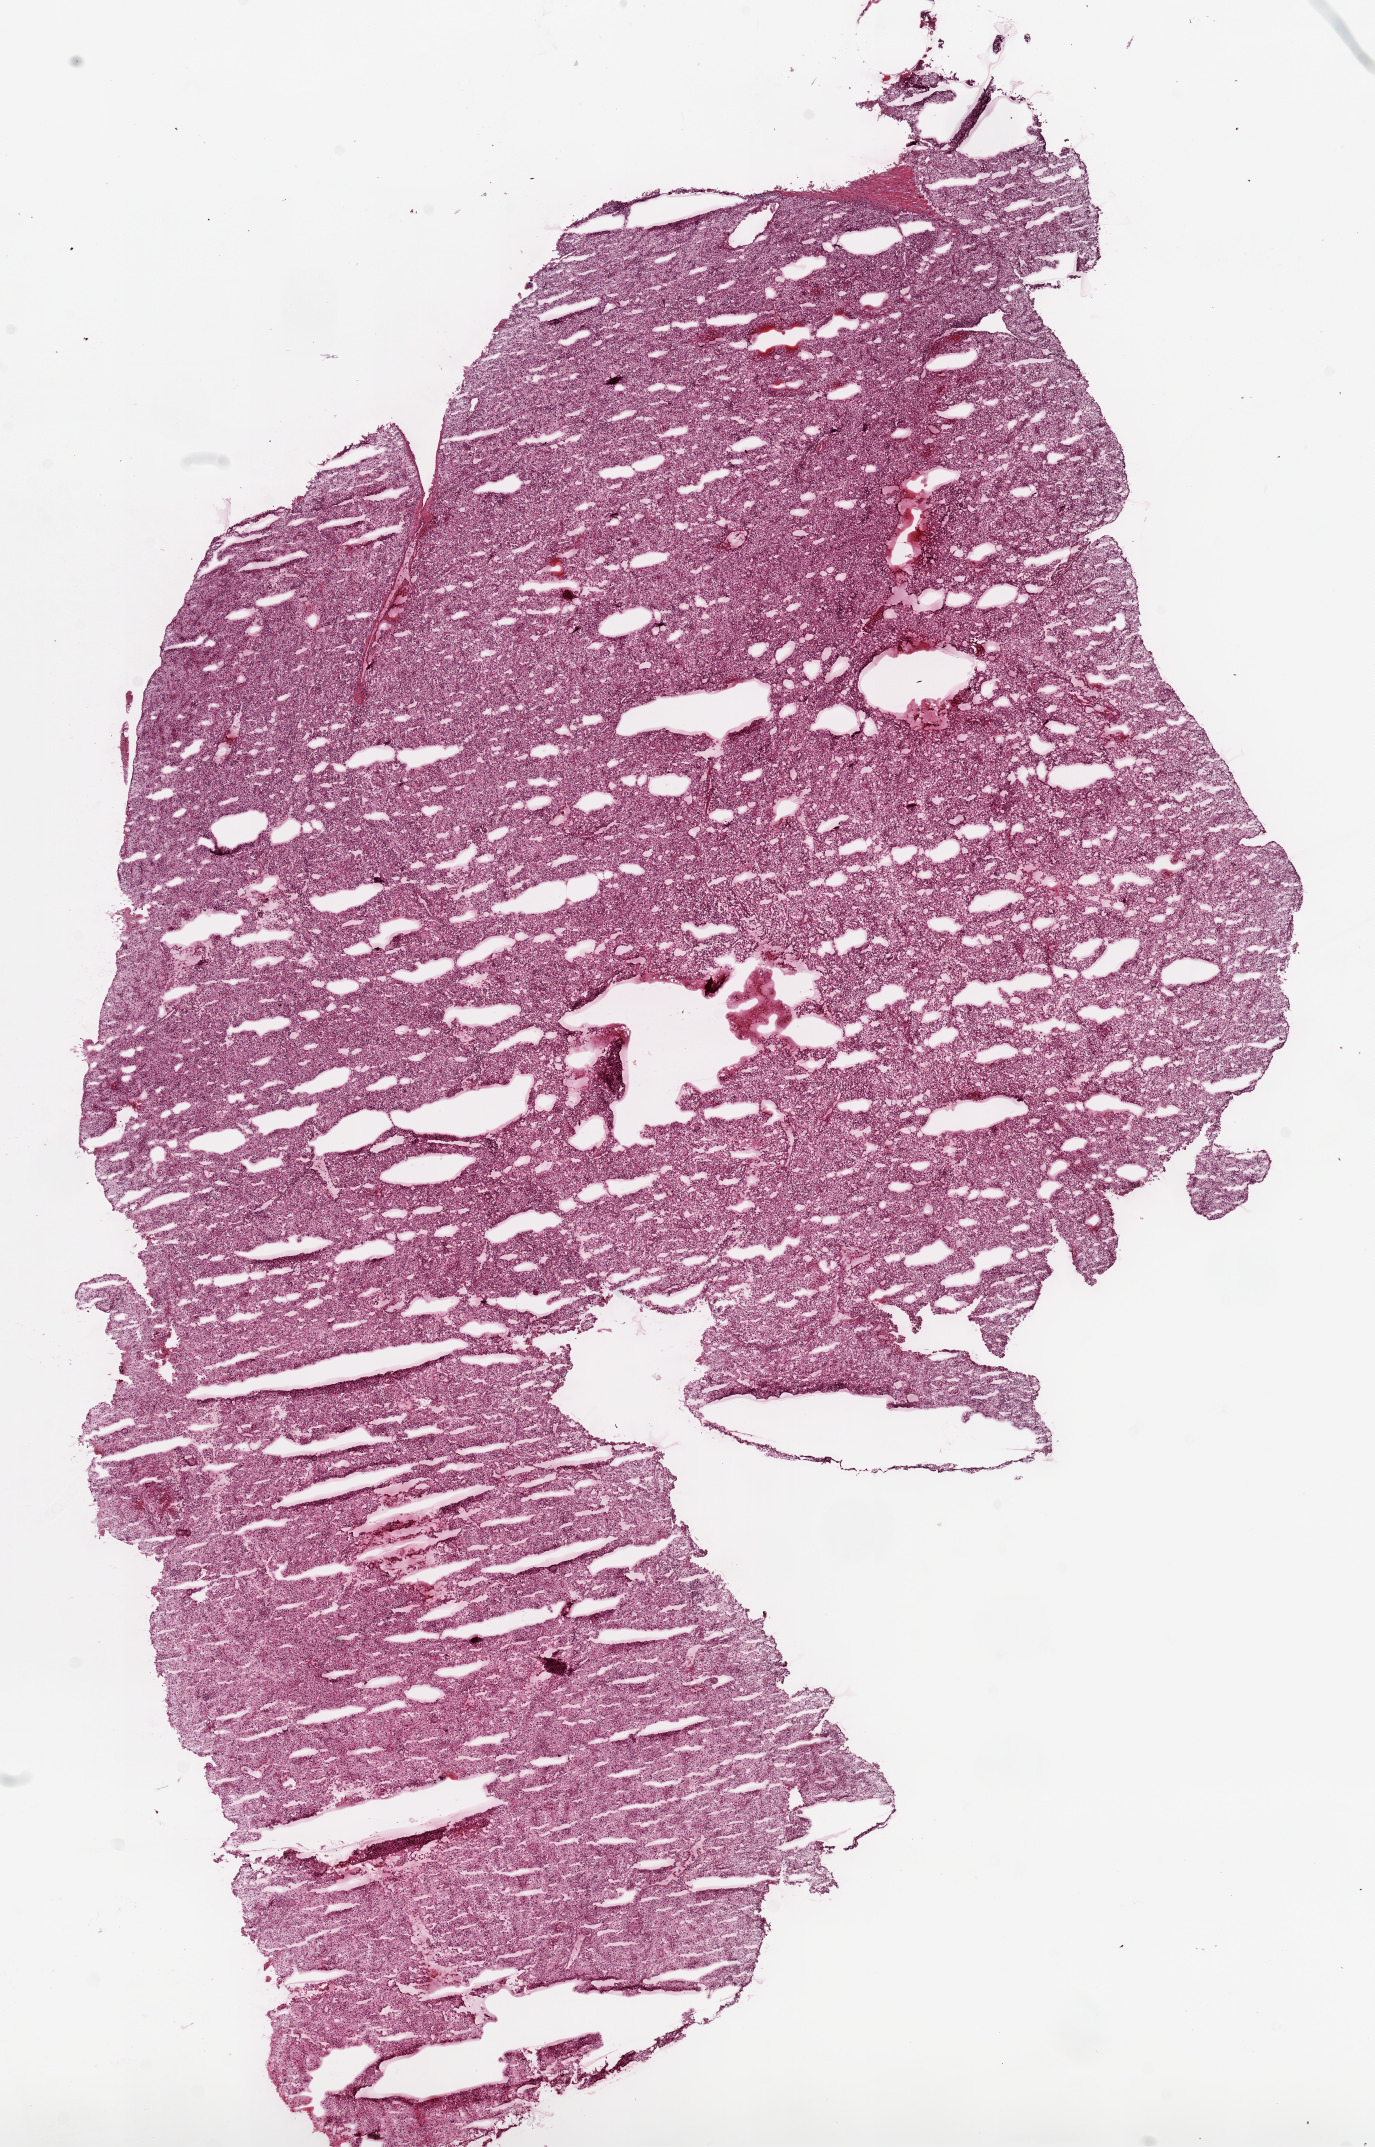
Whole-slide histology image, Hematoxylin and eosin (H&E) stained, shown as a low-resolution overview of the whole scanned area (about 11.0 x 17.2 mm). Frozen section. Primary tumour sample from the kidney. Male, age 53 years at initial diagnosis.
Histologic diagnosis: Clear cell adenocarcinoma, NOS.